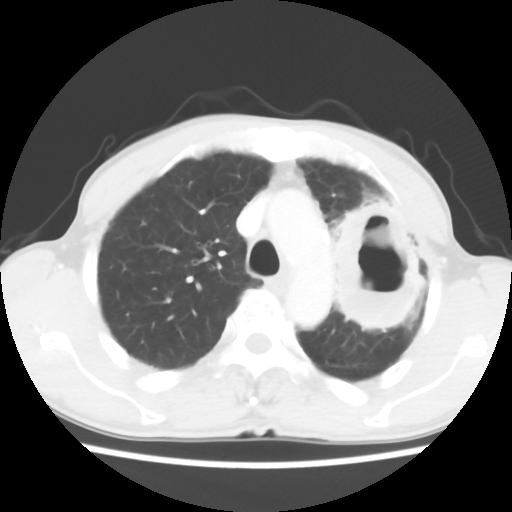
Chest CT, one axial slice; position 44 of 60 along the scan axis; reconstruction kernel STANDARD; lung window (W 1500 / L -600 HU); 5 mm slice thickness; 512 × 512 image matrix. Patient: male, 64 years. From the clinical record (not read from this slice): clinical TNM (as recorded): T3 N3 M0.
Annotated regions visible in this slice (rectangle marked by the reading radiologist):
- lung tumour (recorded histology: adenocarcinoma): box from (x=325, y=189) to (x=427, y=346) px